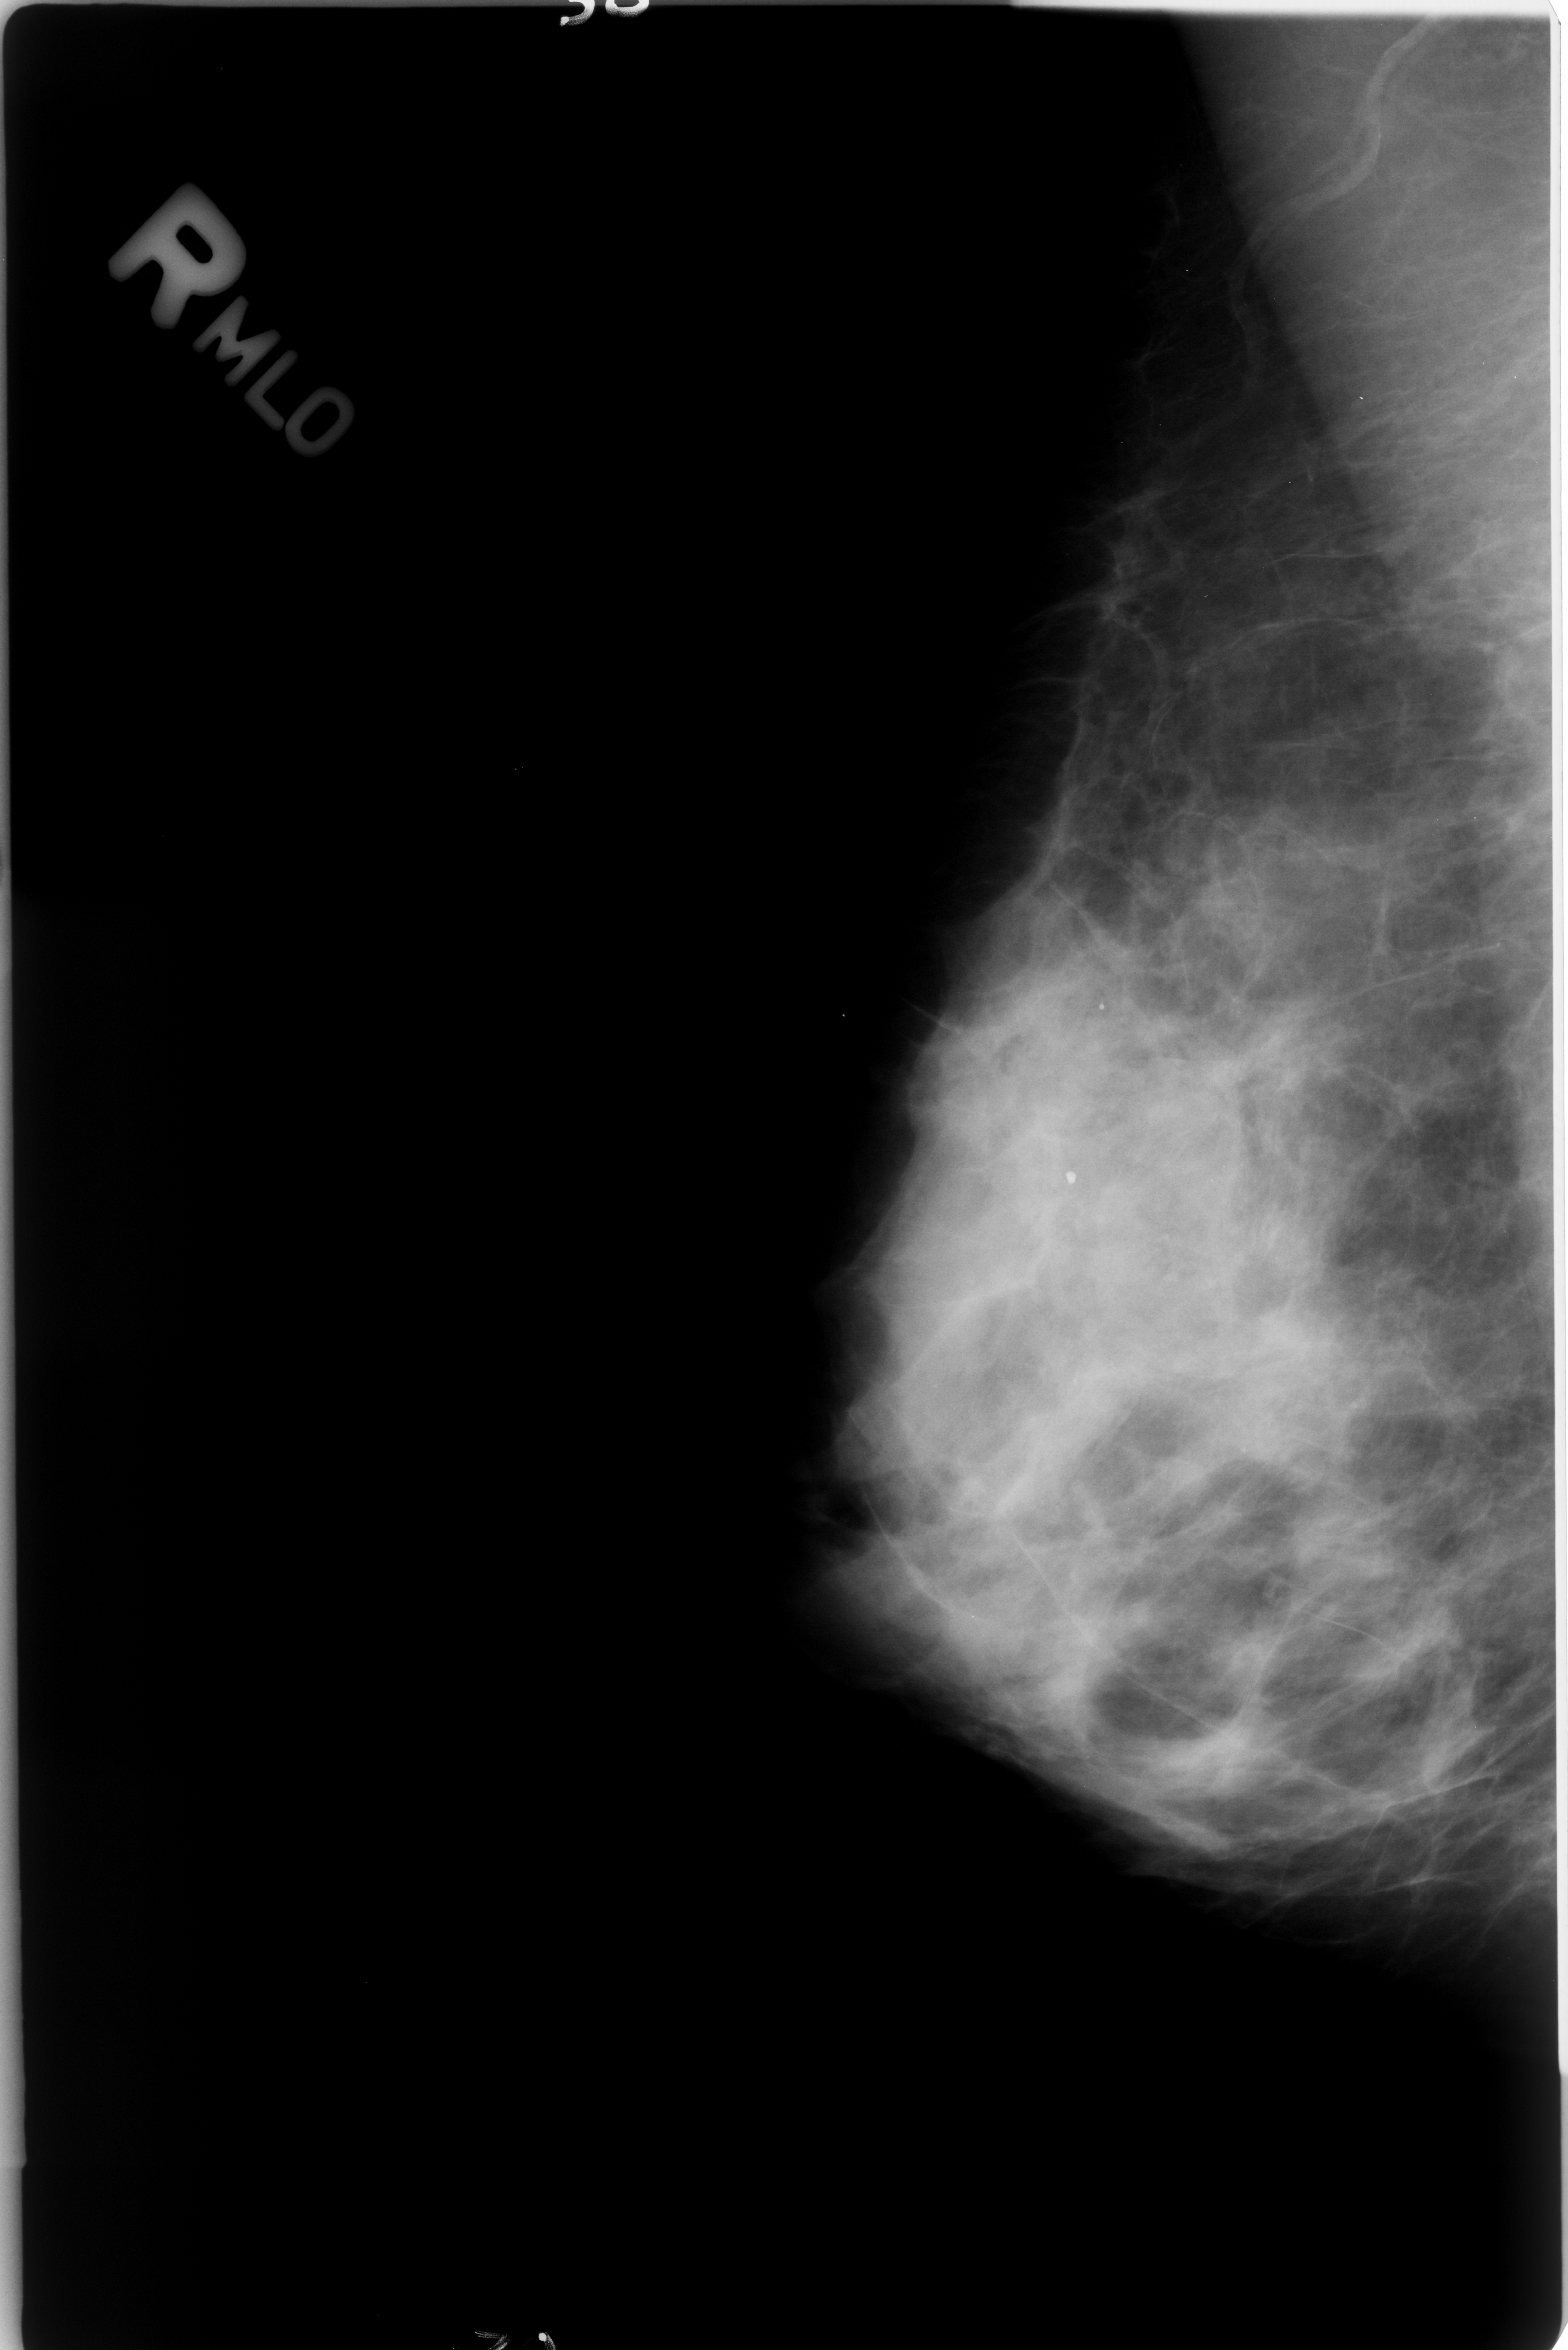
Mammogram (digitized film). Right breast. MLO view. 1568 × 2350 image matrix.
Expert-marked regions of interest on this image (one box per marked abnormality):
- Finding 1 of 2: calcifications, morphology round and regular / lucent center; BI-RADS assessment category 2; subtlety rating 4 on a 1 (subtle) to 5 (obvious) scale; benign; no additional work-up was recommended (outcome (as recorded, no biopsy): benign without callback): bounding box [x1, y1, x2, y2] px = [1057, 1152, 1088, 1199]
- Finding 2 of 2: calcifications, morphology round and regular / lucent center; BI-RADS assessment category 2; subtlety rating 4 on a 1 (subtle) to 5 (obvious) scale; benign; no additional work-up was recommended (outcome (as recorded, no biopsy): benign without callback): [1082, 987, 1120, 1026]